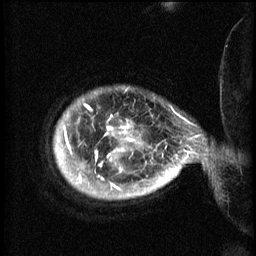
Breast MRI (dynamic contrast-enhanced), one sagittal slice; position 54 of 60 along the scan axis; 3 images stored at this slice position (order not interpretable as contrast timing); 1.5 T; TE 4.2 ms, TR 8.2 ms; 2.3 mm slice thickness; 256 × 256 image matrix. Female patient, age 50 years.
Outlined on this slice (semi-automatically segmented with operator editing):
- analysis volume of interest (the breast-tissue region the enhancement analysis was run in; not a lesion): bounding box [x1, y1, x2, y2] px = [56, 92, 169, 199]
- tumour enhancement mask (voxels above the 70 % enhancement threshold inside the analysis volume of interest): [64, 108, 169, 191]